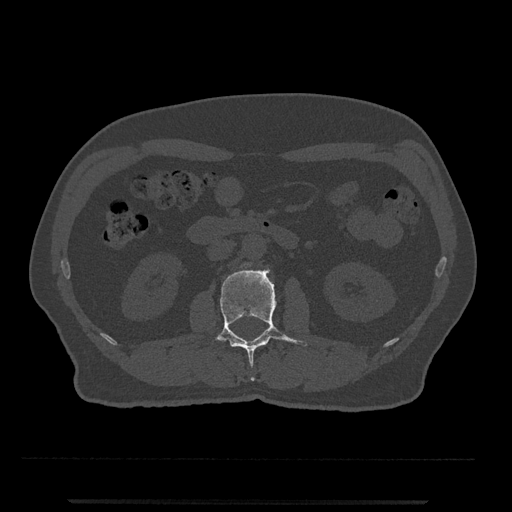
CT including the spine, one axial slice. Position 264 of 797 along the scan axis. Reconstruction kernel Br40s/3. 120 kVp. Bone window (W 1800 / L 400 HU). 512 × 512 image matrix. Male patient, age 63 years. Case-level facts recorded for this patient, not image findings: primary cancer: prostate.
Outlined on this slice (semi-automatically segmented with operator editing):
- L2 vertebra: bounding box (x1, y1, x2, y2) in pixels: (212, 269, 308, 381)